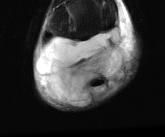
MRI of an extremity soft-tissue mass, one axial slice; position 15 of 81 along the scan axis; T2-weighted fat-saturated; MR volume resampled by the dataset authors to the PET/CT grid (not the native acquisition matrix); 3.27 mm slice thickness; 165 × 137 image matrix, field of view 161 × 134 mm. Male patient. From the clinical record (not read from this slice): histological type: liposarcoma - round cell; grade: high; site of the primary tumour: right calf.
Outlined on this slice (expert contour drawn on MRI and transferred to this co-registered scan by the dataset authors):
- gross tumour volume (mass): box from (x=37, y=27) to (x=131, y=106) px